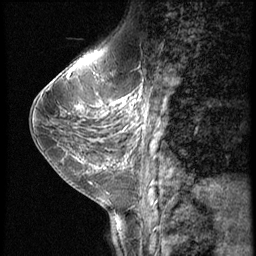
Breast MRI (dynamic contrast-enhanced), one sagittal slice. Position 25 of 56 along the scan axis. Dynamic contrast-enhanced series, image 2 of 3 at this slice position (ordered by acquisition). 1.5 T. TE 4.2 ms, TR 9 ms. 2.5 mm slice thickness. 256 × 256 image matrix, field of view 180 × 180 mm. Patient: female, 38 years. From the clinical record (not read from this slice): setting: breast cancer imaged before/during neoadjuvant chemotherapy; receptor status: triple-negative.
Annotated regions visible in this slice (semi-automatically segmented with operator editing):
- analysis volume of interest (the breast-tissue region the enhancement analysis was run in; not a lesion): box from (x=107, y=95) to (x=150, y=149) px
- tumour enhancement mask (voxels above the 140 % enhancement threshold inside the analysis volume of interest): (x=112, y=98)–(x=136, y=113)